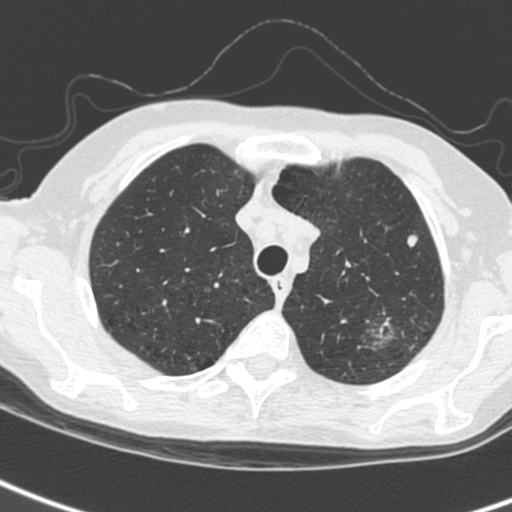
Axial slice from a low-dose chest CT screening exam, baseline screening round, lung window (W 1500 / L -600 HU), 1.3 mm slice thickness, 120 kVp, slice 35 of 242 in the series. Female participant, aged 61 years at enrolment. Current smoker at enrolment.
- 2 expert-annotated lung lesions on this slice (largest first), box from (x=354, y=307) to (x=412, y=352) px; (x=395, y=225)–(x=430, y=256).
- The screening reader recorded 2 non-calcified nodules or masses ≥4 mm on this exam (left upper lobe, left upper lobe); which of them these boxes mark is not recorded.